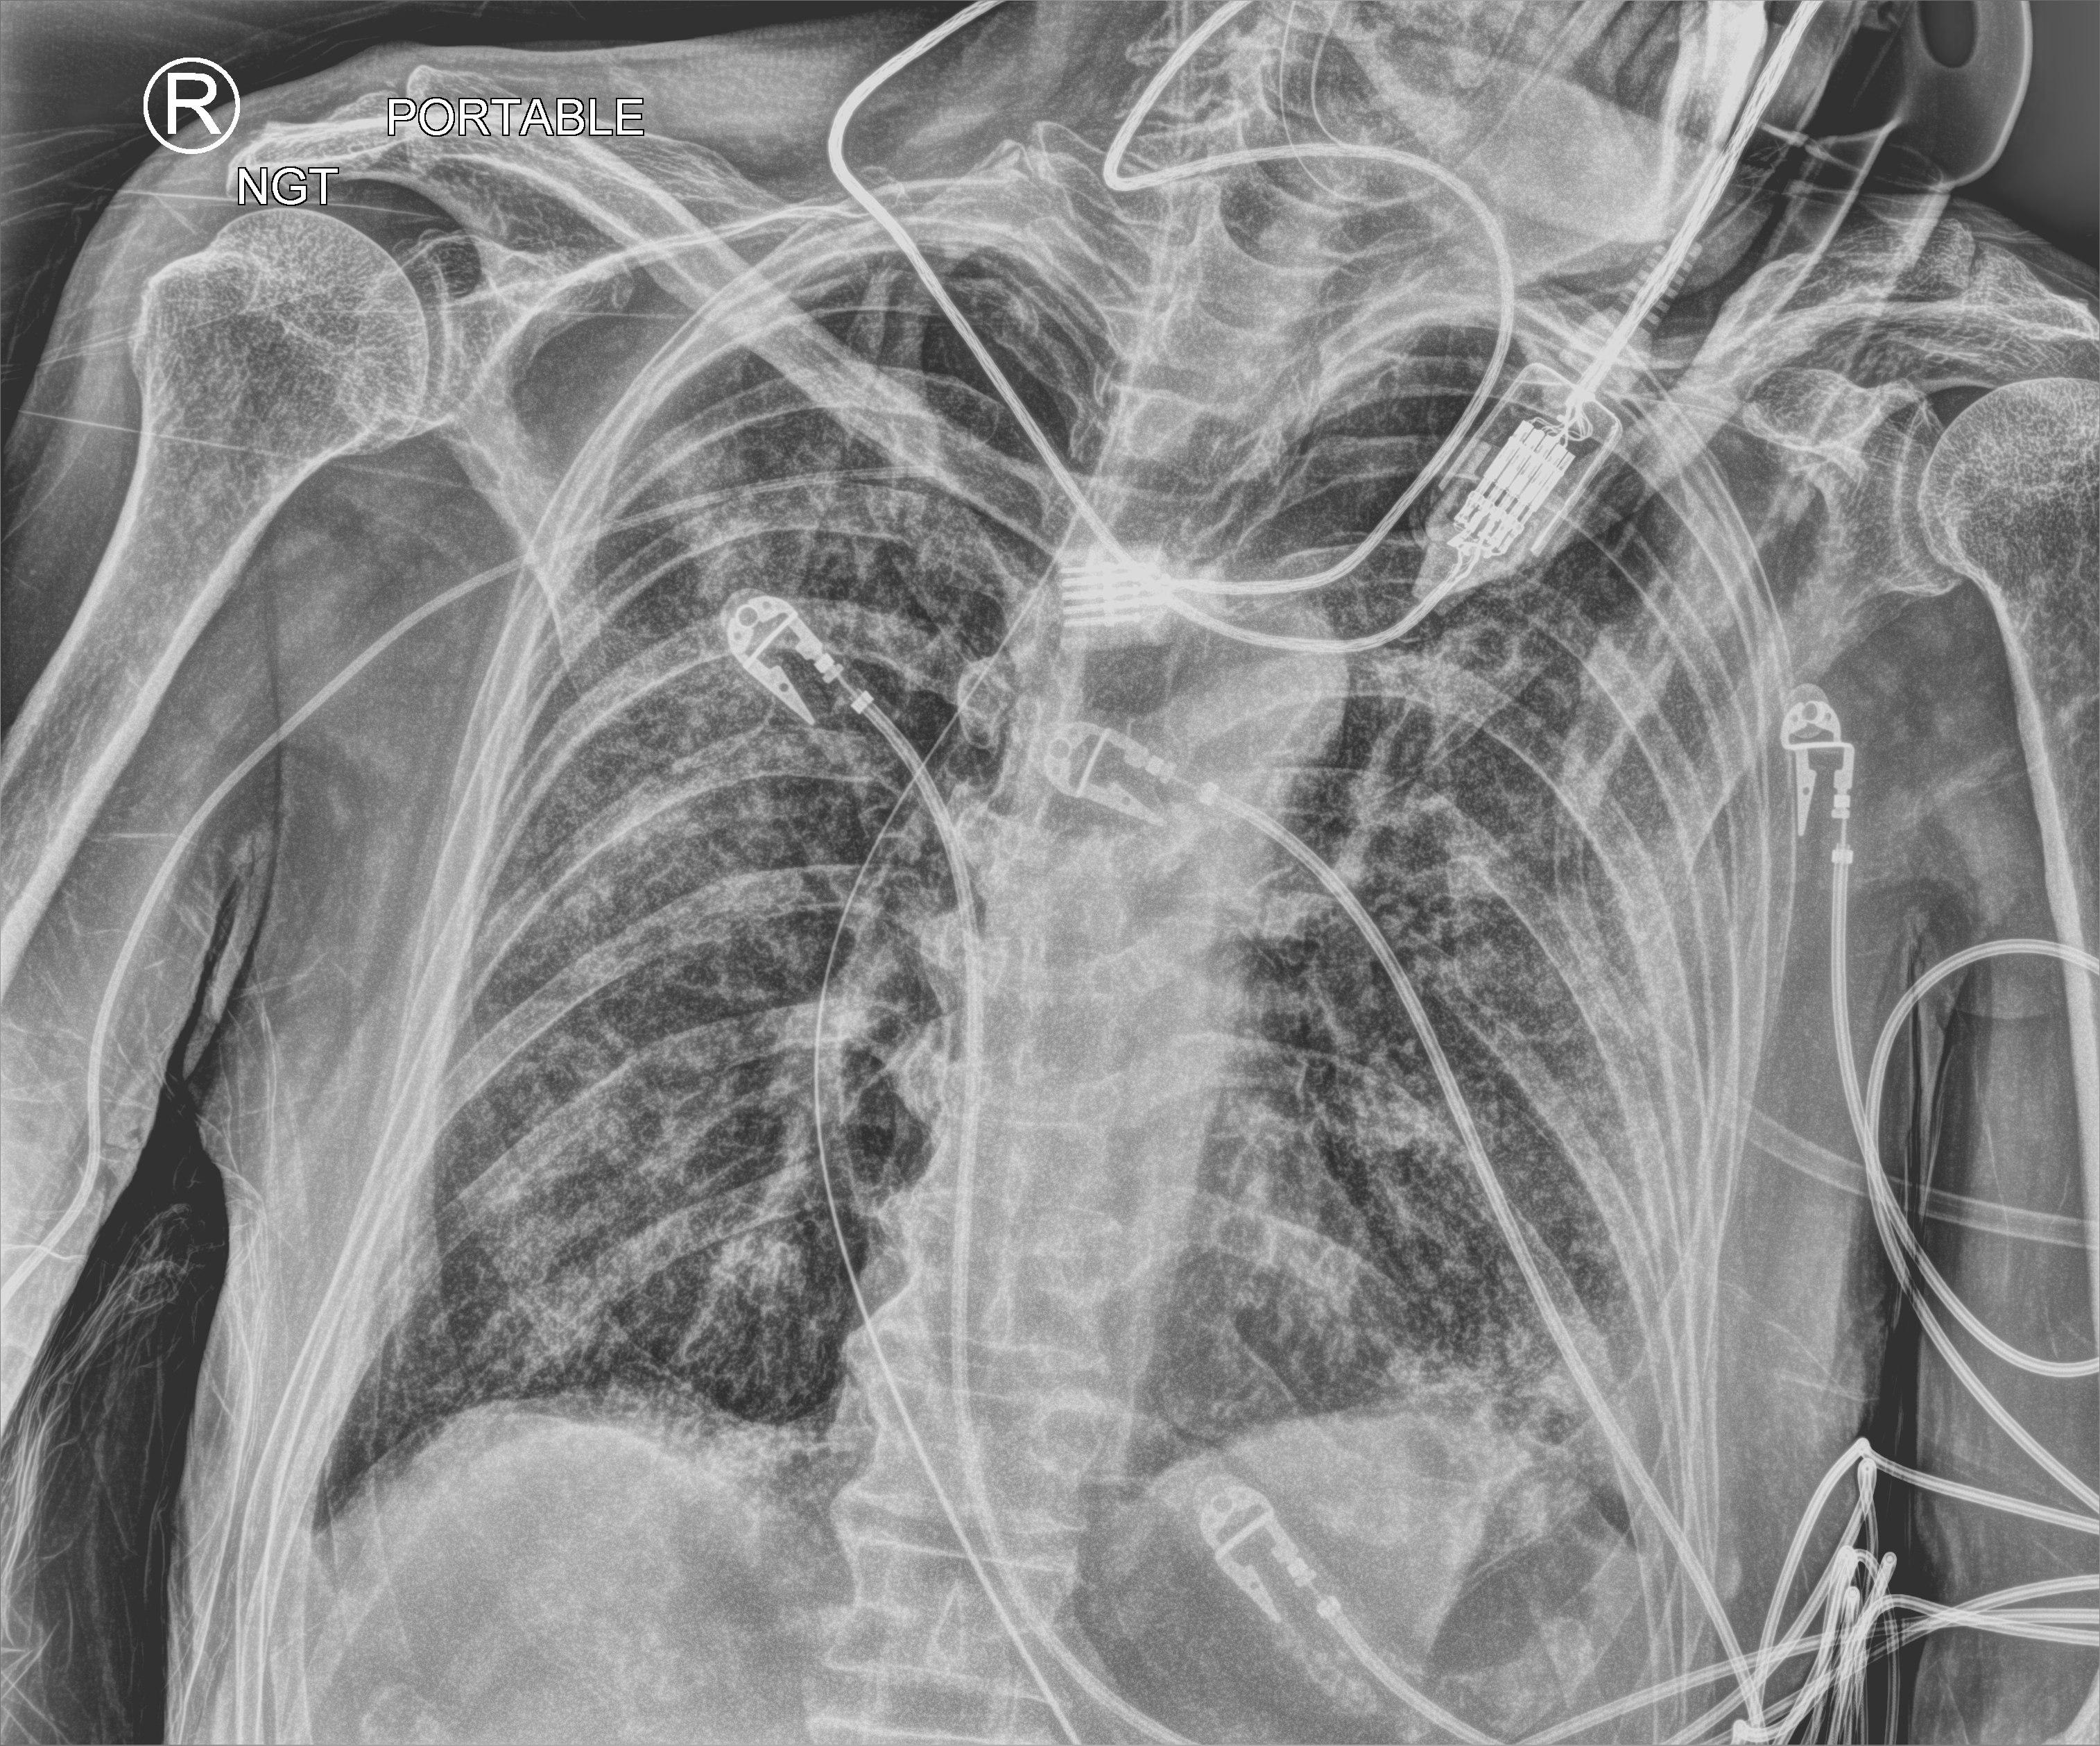
Bedside chest radiograph (computed radiography). Patient hospitalised with COVID-19; male, aged 60–74 years.
From the hospital-stay record, not from the radiograph (when in the stay this image was taken is not recorded): length of hospital stay: 42 days; admitted to intensive care during this hospital stay: yes; mechanically ventilated during this hospital stay: yes.